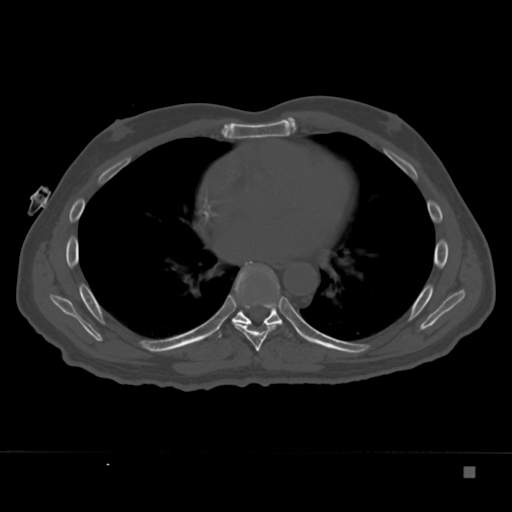
CT including the spine, one axial slice. Slice 216 of 332 in the series (ordered by position). 120 kVp. Bone window (W 1800 / L 400 HU). 512 × 512 image matrix. Patient: male, 72 years. Case-level facts recorded for this patient, not image findings: primary cancer: skeletal.
Structures marked on this image (semi-automatic segmentation, software-assisted and operator-edited):
- T7 vertebra: box from (x=235, y=261) to (x=280, y=352) px
- T8 vertebra: (x=217, y=268)–(x=302, y=338)